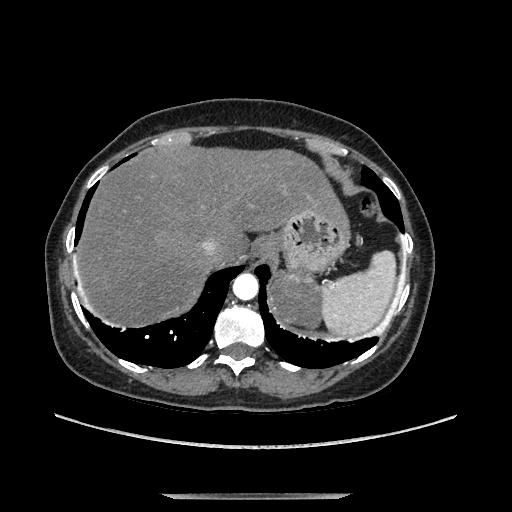
Contrast-enhanced abdominal CT, one axial slice. Slice 114 of 169 in the series (ordered by position). Soft-tissue window (W 400 / L 40 HU). 1.25 mm slice thickness. 512 × 512 image matrix, field of view 400 × 400 mm. Female patient. Case-level facts recorded for this patient, not image findings: diagnosis: adrenocortical carcinoma; tumour side: left adrenal; tumour size at pathology: 9 cm; Ki-67 index: 2 %; stage (as recorded): 3.
Structures marked on this image (semi-automatic segmentation, software-assisted and operator-edited):
- mass: bounding box [x1, y1, x2, y2] px = [275, 277, 321, 325]